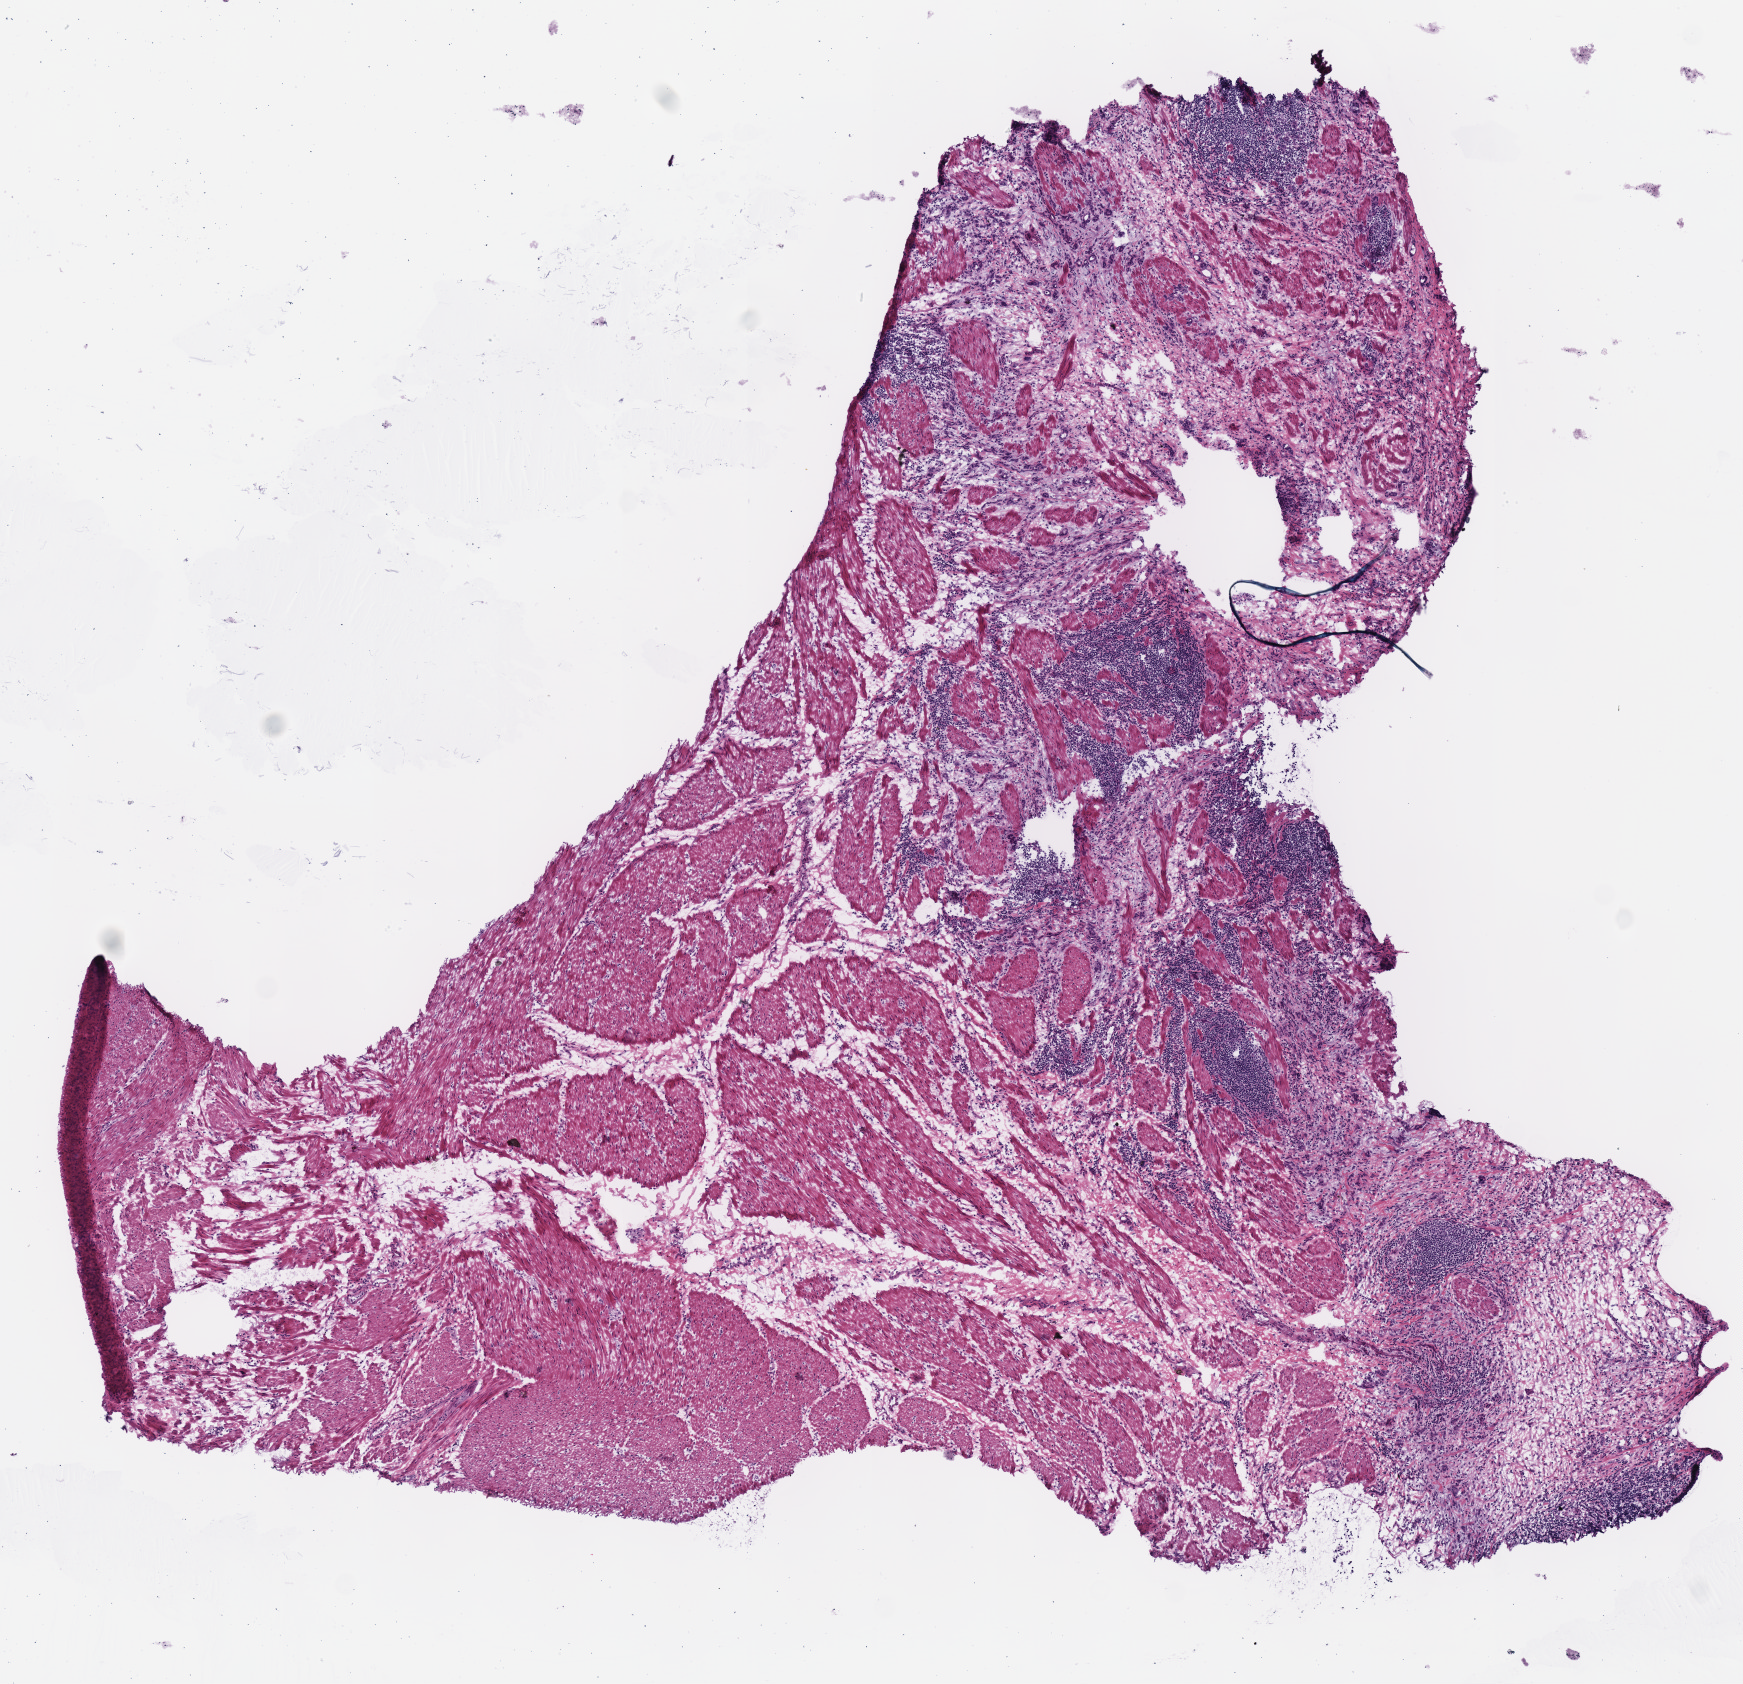
Digitized Hematoxylin and eosin (H&E) stained tissue section (whole slide), whole scanned area (about 6.9 x 6.6 mm) shown as a low-resolution overview, frozen section from the top of the tissue portion, stomach, primary tumour sample. Patient: male, age at initial diagnosis 49 years.
Pathologic diagnosis: Carcinoma, diffuse type (gastric antrum).